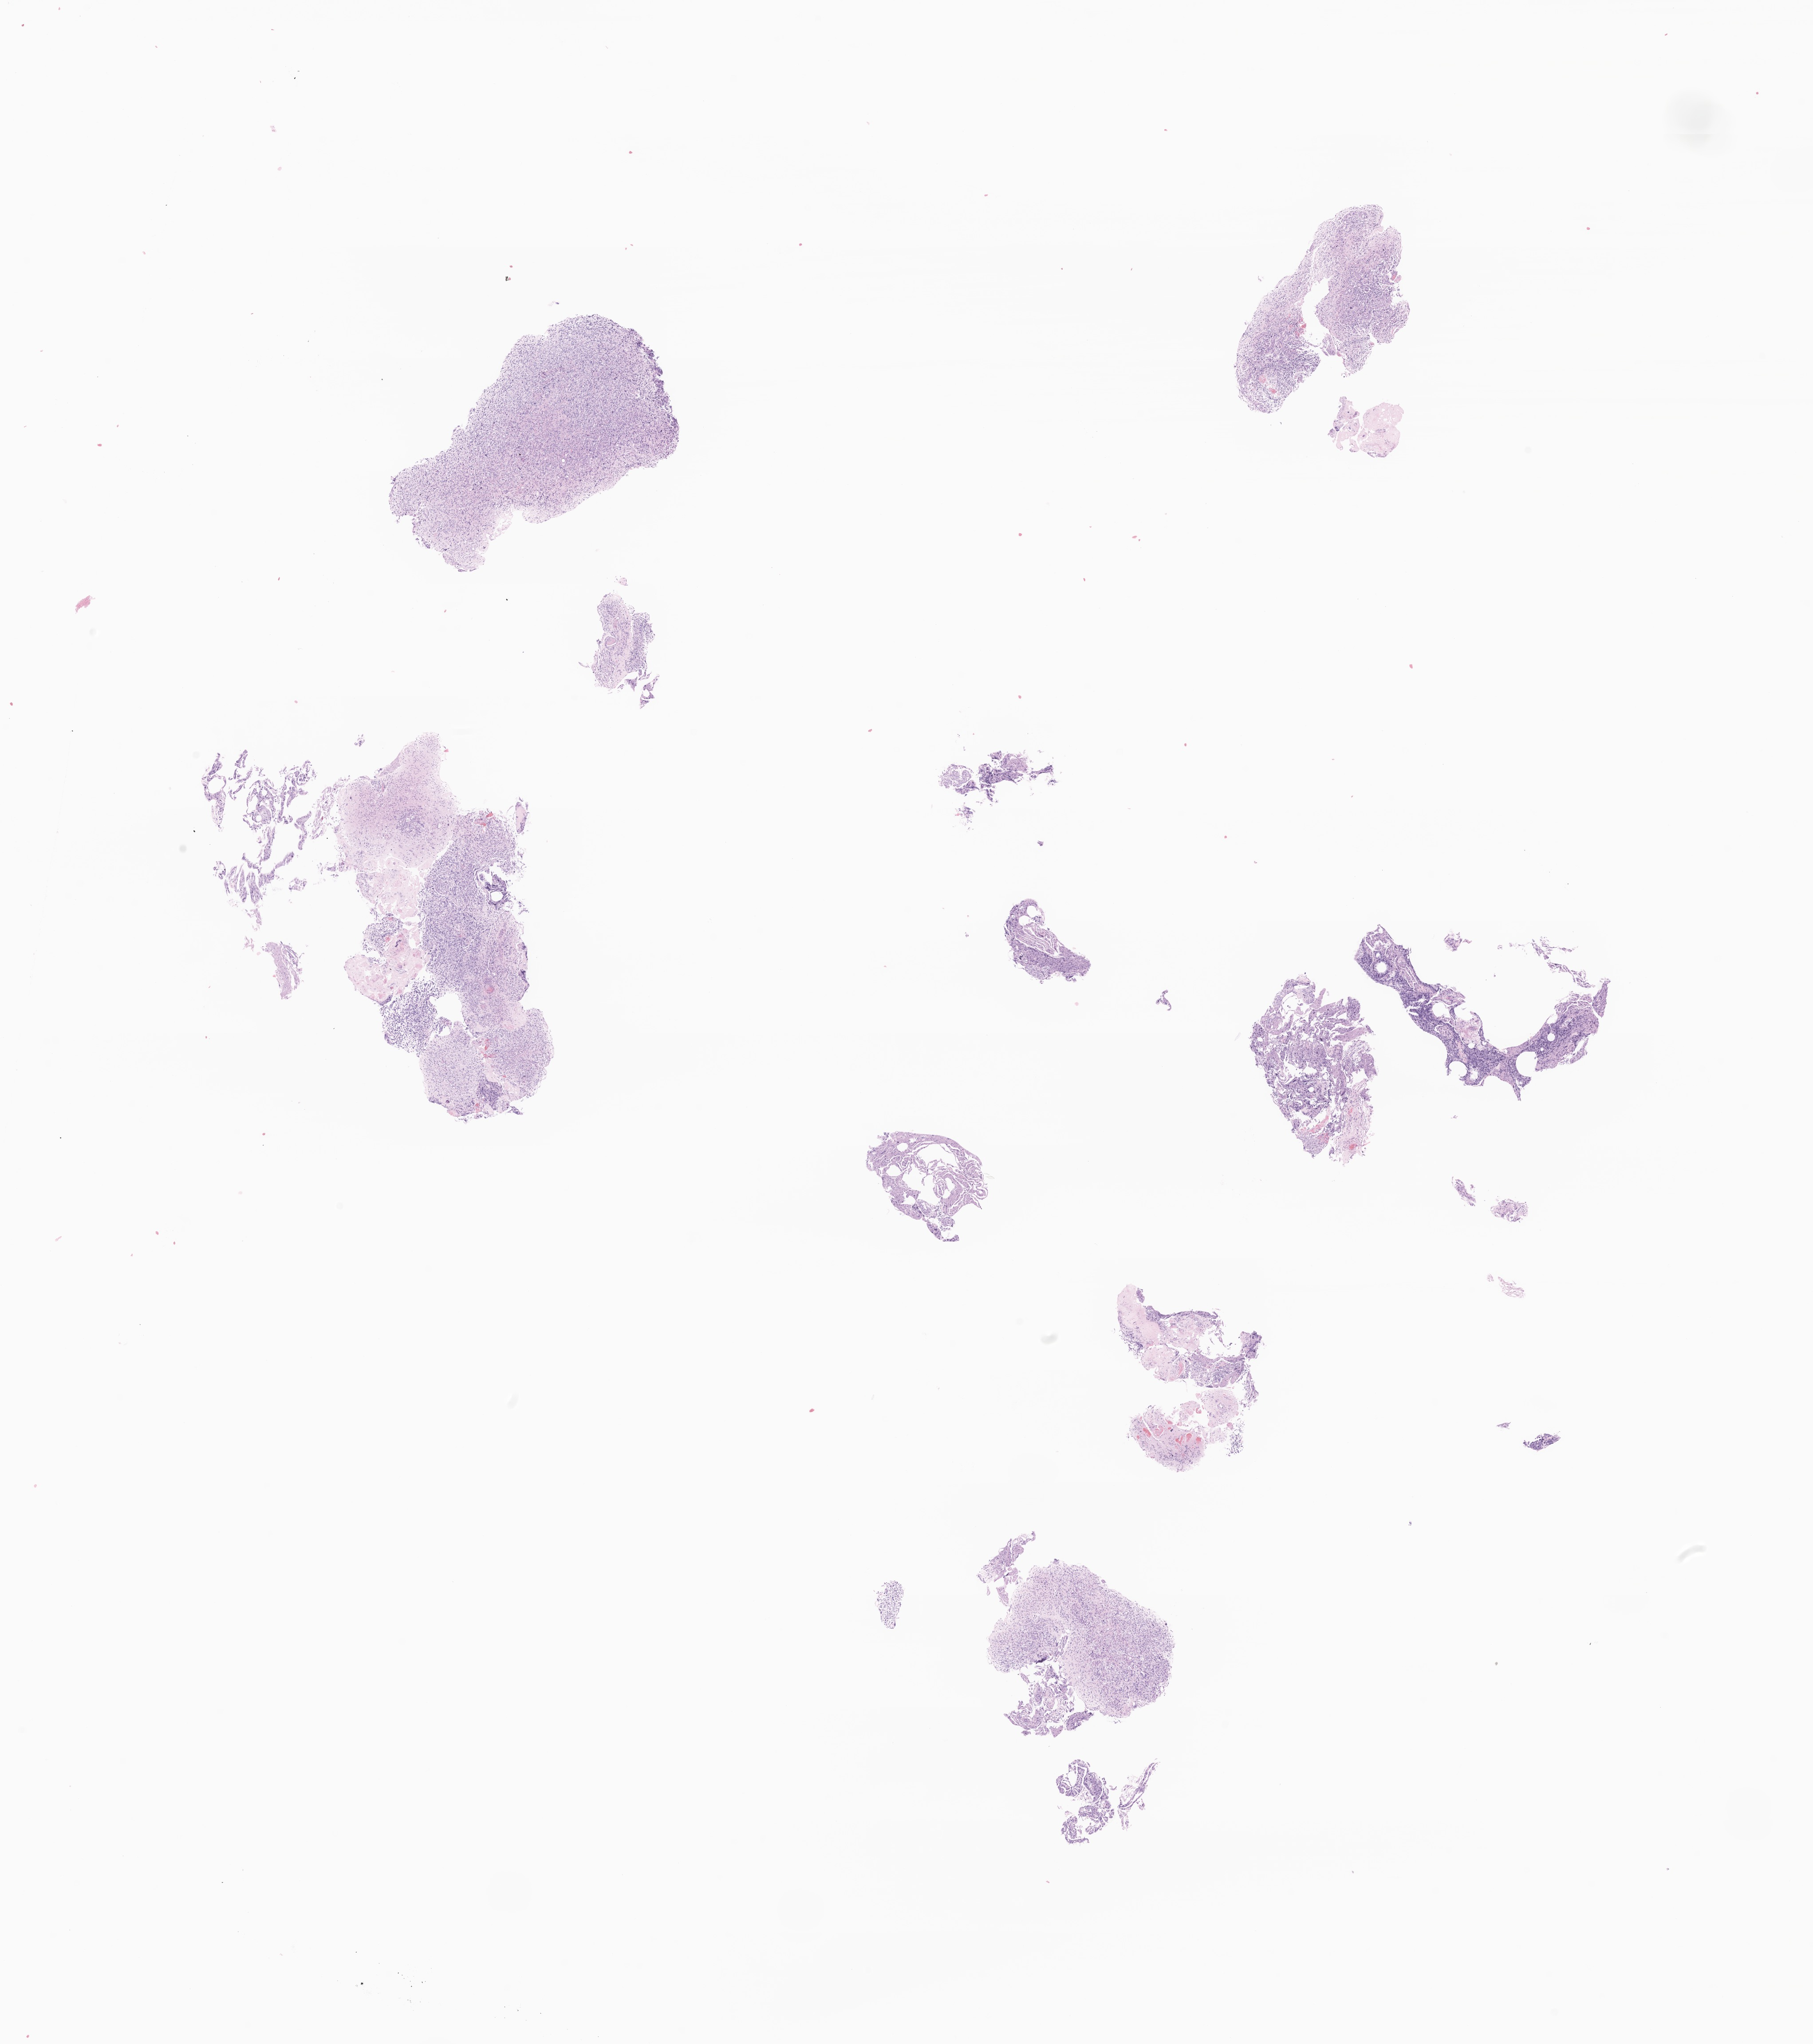
Digitized H&E-stained section of tumor tissue from the spinal cord, shown as a low-resolution overview of the whole scanned area (about 17.2 x 19.4 mm); formalin-fixed, paraffin-embedded (FFPE) tissue. Male patient, age 174 months (14 years 6 months).
Recorded diagnosis: Neoplasm, uncertain whether benign or malignant.